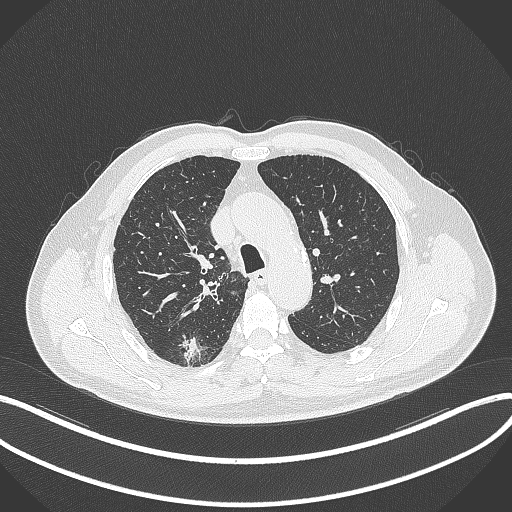
Chest CT, one axial slice; slice 269 of 359 in the series (ordered by position); reconstruction kernel B70f; lung window (W 1500 / L -600 HU); 1 mm slice thickness; 512 × 512 image matrix. Patient: male, 69 years. Case-level facts recorded for this patient, not image findings: clinical TNM (as recorded): T1b N0 M0; histopathological grade: G2-3.
Structures marked on this image (bounding box drawn by a radiologist):
- lung tumour (recorded histology: adenocarcinoma): bounding box <179,332,203,366> (left, top, right, bottom; pixels)